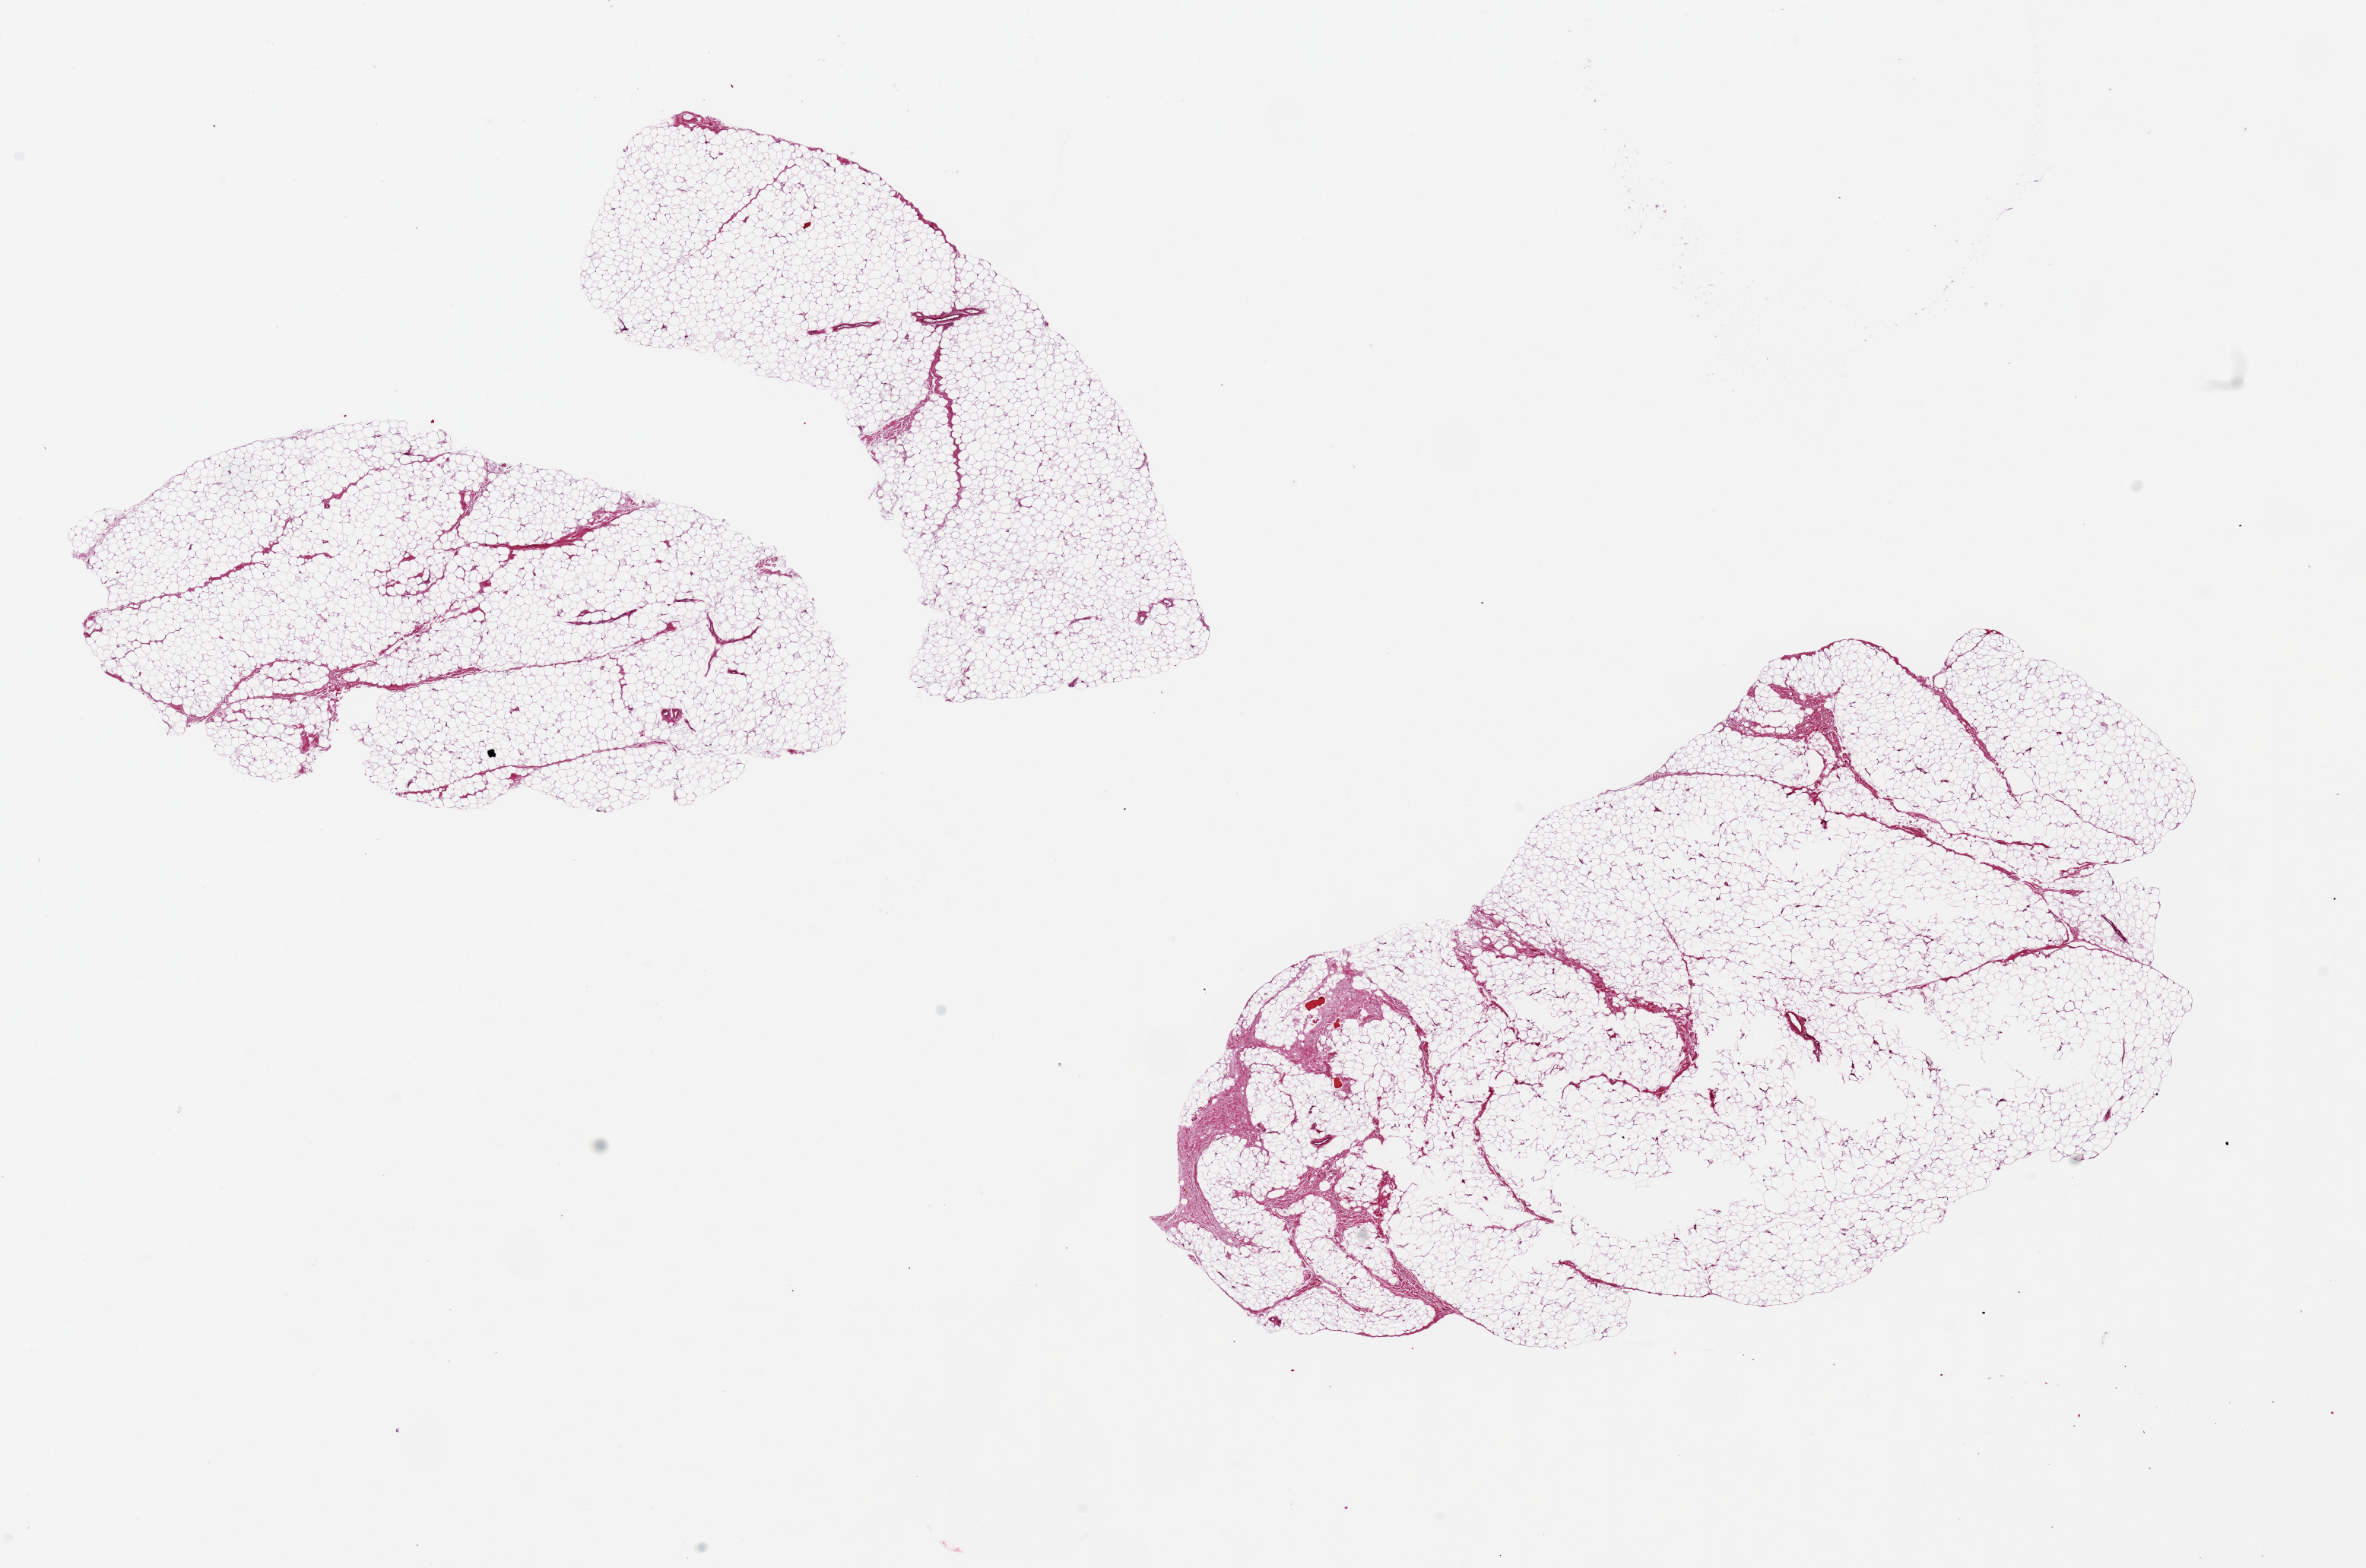
Digitized H&E-stained section — shown as a low-resolution overview of the whole scanned area (about 24.6 x 16.3 mm, acquisition: 20x scan), PAXgene-fixed paraffin-embedded (PFPE) section, section of breast (target tissue), tissue donor sample. Donor sex: male.
• pathologist's review note for this sample: 2 pieces, 9x7 & 11x6mm; all fibroadipose, not ductal elements noted